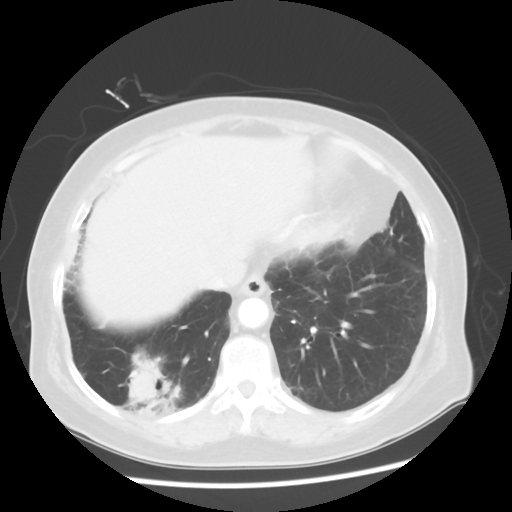
Chest CT, one axial slice. Slice 15 of 56 in the series (ordered by position). Reconstruction kernel STANDARD. 120 kVp. Lung window (W 1500 / L -600 HU). 5 mm slice thickness. 512 × 512 image matrix, field of view 360 × 360 mm. Female patient, age 64 years. From the clinical record (not read from this slice): clinical TNM (as recorded): Tis N0 M0.
Annotated regions visible in this slice (bounding box drawn by a radiologist):
- lung tumour (recorded histology: adenocarcinoma): bounding box (x1, y1, x2, y2) in pixels: (122, 347, 181, 426)